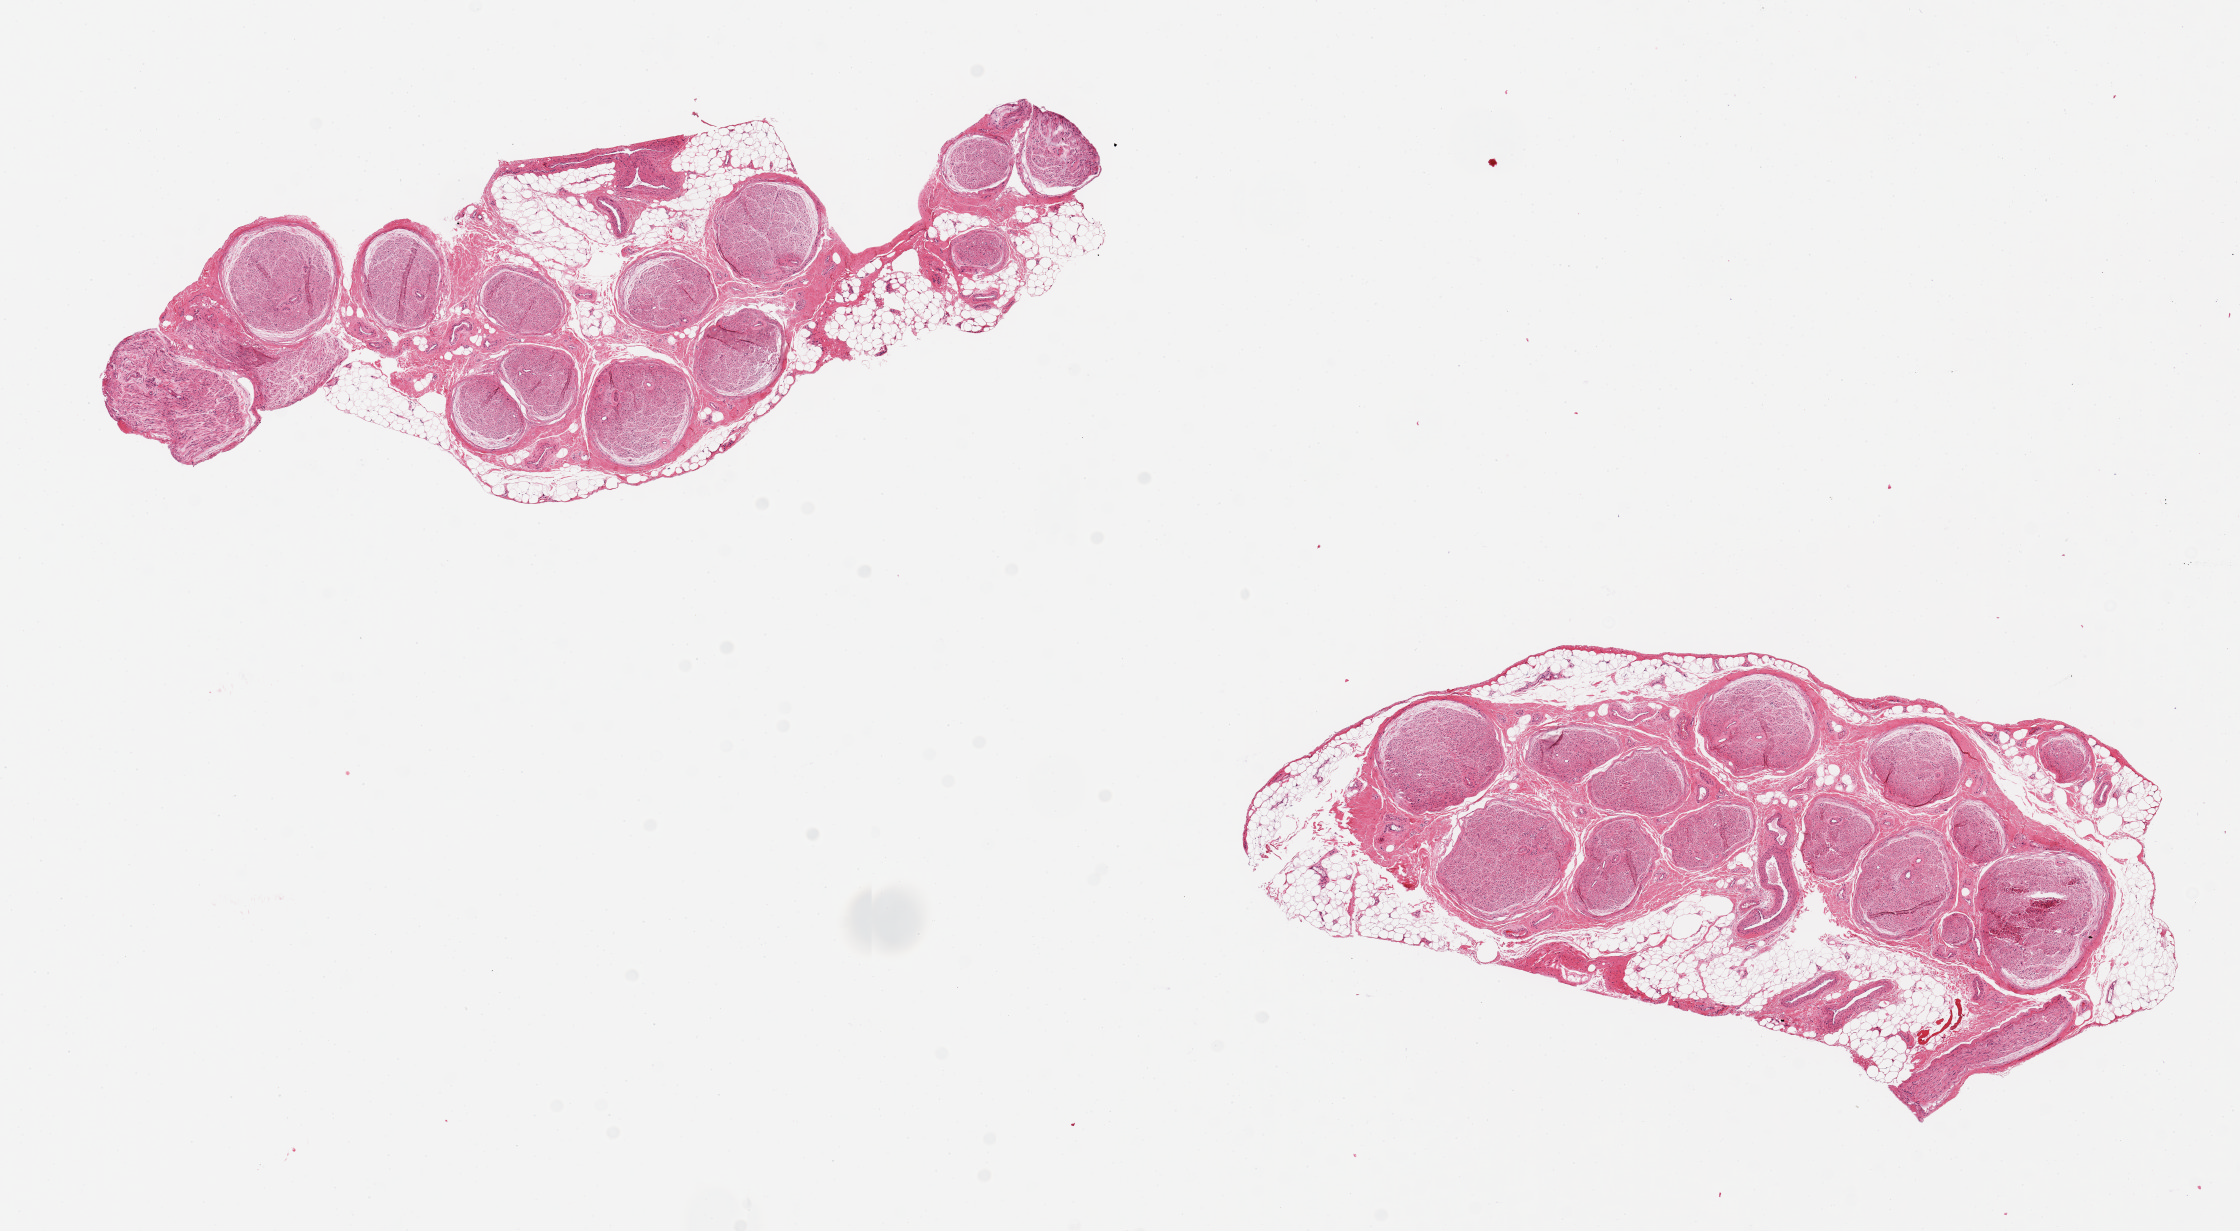
Digitized H&E-stained section — low-resolution overview of the scanned area, about 17.7 x 9.7 mm. PAXgene-fixed, paraffin-embedded tissue. Sampled site (target tissue): tibial nerve. Tissue donor sample. Donor: male.
* reviewer comment on this tissue sample: 2 pieces, 8x3 & 7x4mm; Small arteries are sclerotic. (Hypertension, diabetes-history). 30% peripheral adipose